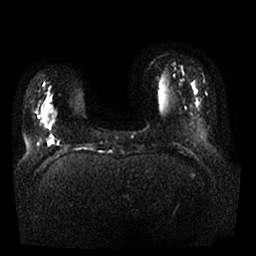
Breast MRI, one axial slice. Position 3 of 25 along the scan axis. Diffusion-weighted series; image 2 of 4 stored at this slice position (different b-values; order by instance number). 1.5 T. 4 mm slice thickness. 256 × 256 image matrix, field of view 350 × 350 mm. Female patient.
Outlined on this slice (manually delineated by an expert):
- tumour on diffusion-weighted imaging: bounding box (x1, y1, x2, y2) in pixels: (41, 103, 55, 128)